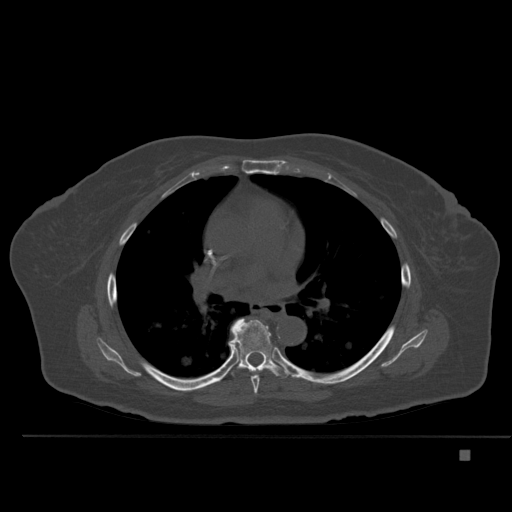
CT including the spine, one axial slice. Slice 331 of 477 in the series (ordered by position). Bone window (W 1800 / L 400 HU). 1.5 mm slice thickness. 512 × 512 image matrix, field of view 422 × 422 mm. Female patient, age 74 years. Case-level facts recorded for this patient, not image findings: primary cancer: colon.
Annotated regions visible in this slice (semi-automatically segmented with operator editing):
- T6 vertebra: box from (x=251, y=368) to (x=268, y=394) px
- T7 vertebra: (x=229, y=318)–(x=291, y=378)